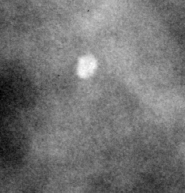
Region of interest cut from a scanned film mammogram (one marked finding), right breast, CC view, BI-RADS breast density category 3 (scale 1–4).
- Marked abnormality: calcifications, morphology lucent center; BI-RADS assessment category 2; subtlety rating 5 on a 1 (subtle) to 5 (obvious) scale; benign; no additional work-up was recommended (benign without callback).